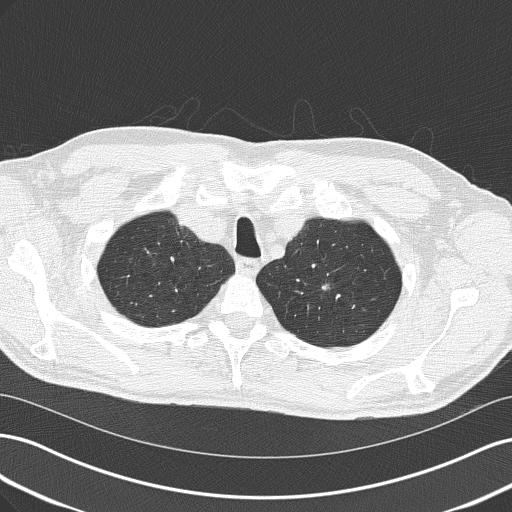
Axial slice from a low-dose chest CT screening exam, second screening round (one year after baseline), lung window (W 1500 / L -600 HU), 2 mm slice thickness, slice 39 of 185 in the series, 512 × 512 image matrix, field of view 360 × 360 mm. Male participant, aged 64 years at enrolment. Former smoker at enrolment.
Lesion marked by an expert reader, bounding box <305,267,338,306> (left, top, right, bottom; pixels). The screening reader recorded 2 non-calcified nodules or masses ≥4 mm on this exam; which of them this box marks is not recorded. Official screen result: positive, no significant change: stable abnormalities potentially related to lung cancer, unchanged since the prior screening exam. Participant outcome: lung cancer diagnosed 482 days after this screen (after the third annual screen) — adenocarcinoma, NOS, left upper lobe, poorly differentiated (G3), stage IA (AJCC 6th edition), 10 mm at pathology.